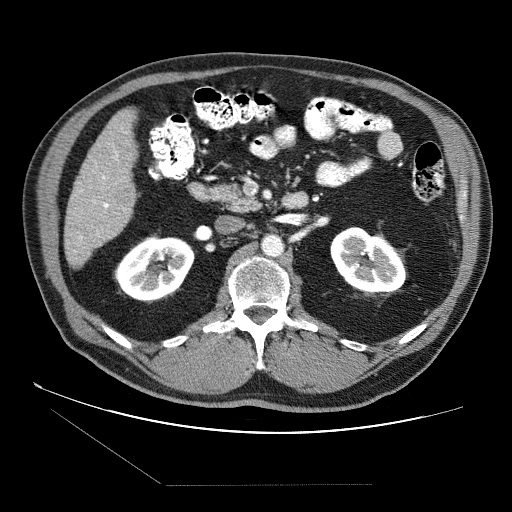
Contrast-enhanced abdominal CT (liver protocol), one axial slice. Position 20 of 87 along the scan axis. Reconstruction kernel STANDARD. 120 kVp. Soft-tissue window (W 400 / L 40 HU). 2.5 mm slice thickness. 512 × 512 image matrix, field of view 400 × 400 mm. Case-level facts recorded for this patient, not image findings: diagnosis: hepatocellular carcinoma (patient treated with transarterial chemoembolisation; whether this scan precedes or follows treatment is not stated here); TNM stage (as recorded): Stage-II; Child-Pugh class: B; tumour nodularity: multinodular; tumour size: 2.6 cm.
Annotated regions visible in this slice (semi-automatically segmented with operator editing):
- liver parenchyma outside the tumour (the mass and vessels are separate outlines, so this box may not span the whole liver): bounding box <64,108,136,268> (left, top, right, bottom; pixels)
- liver vessels: <79,132,126,240>